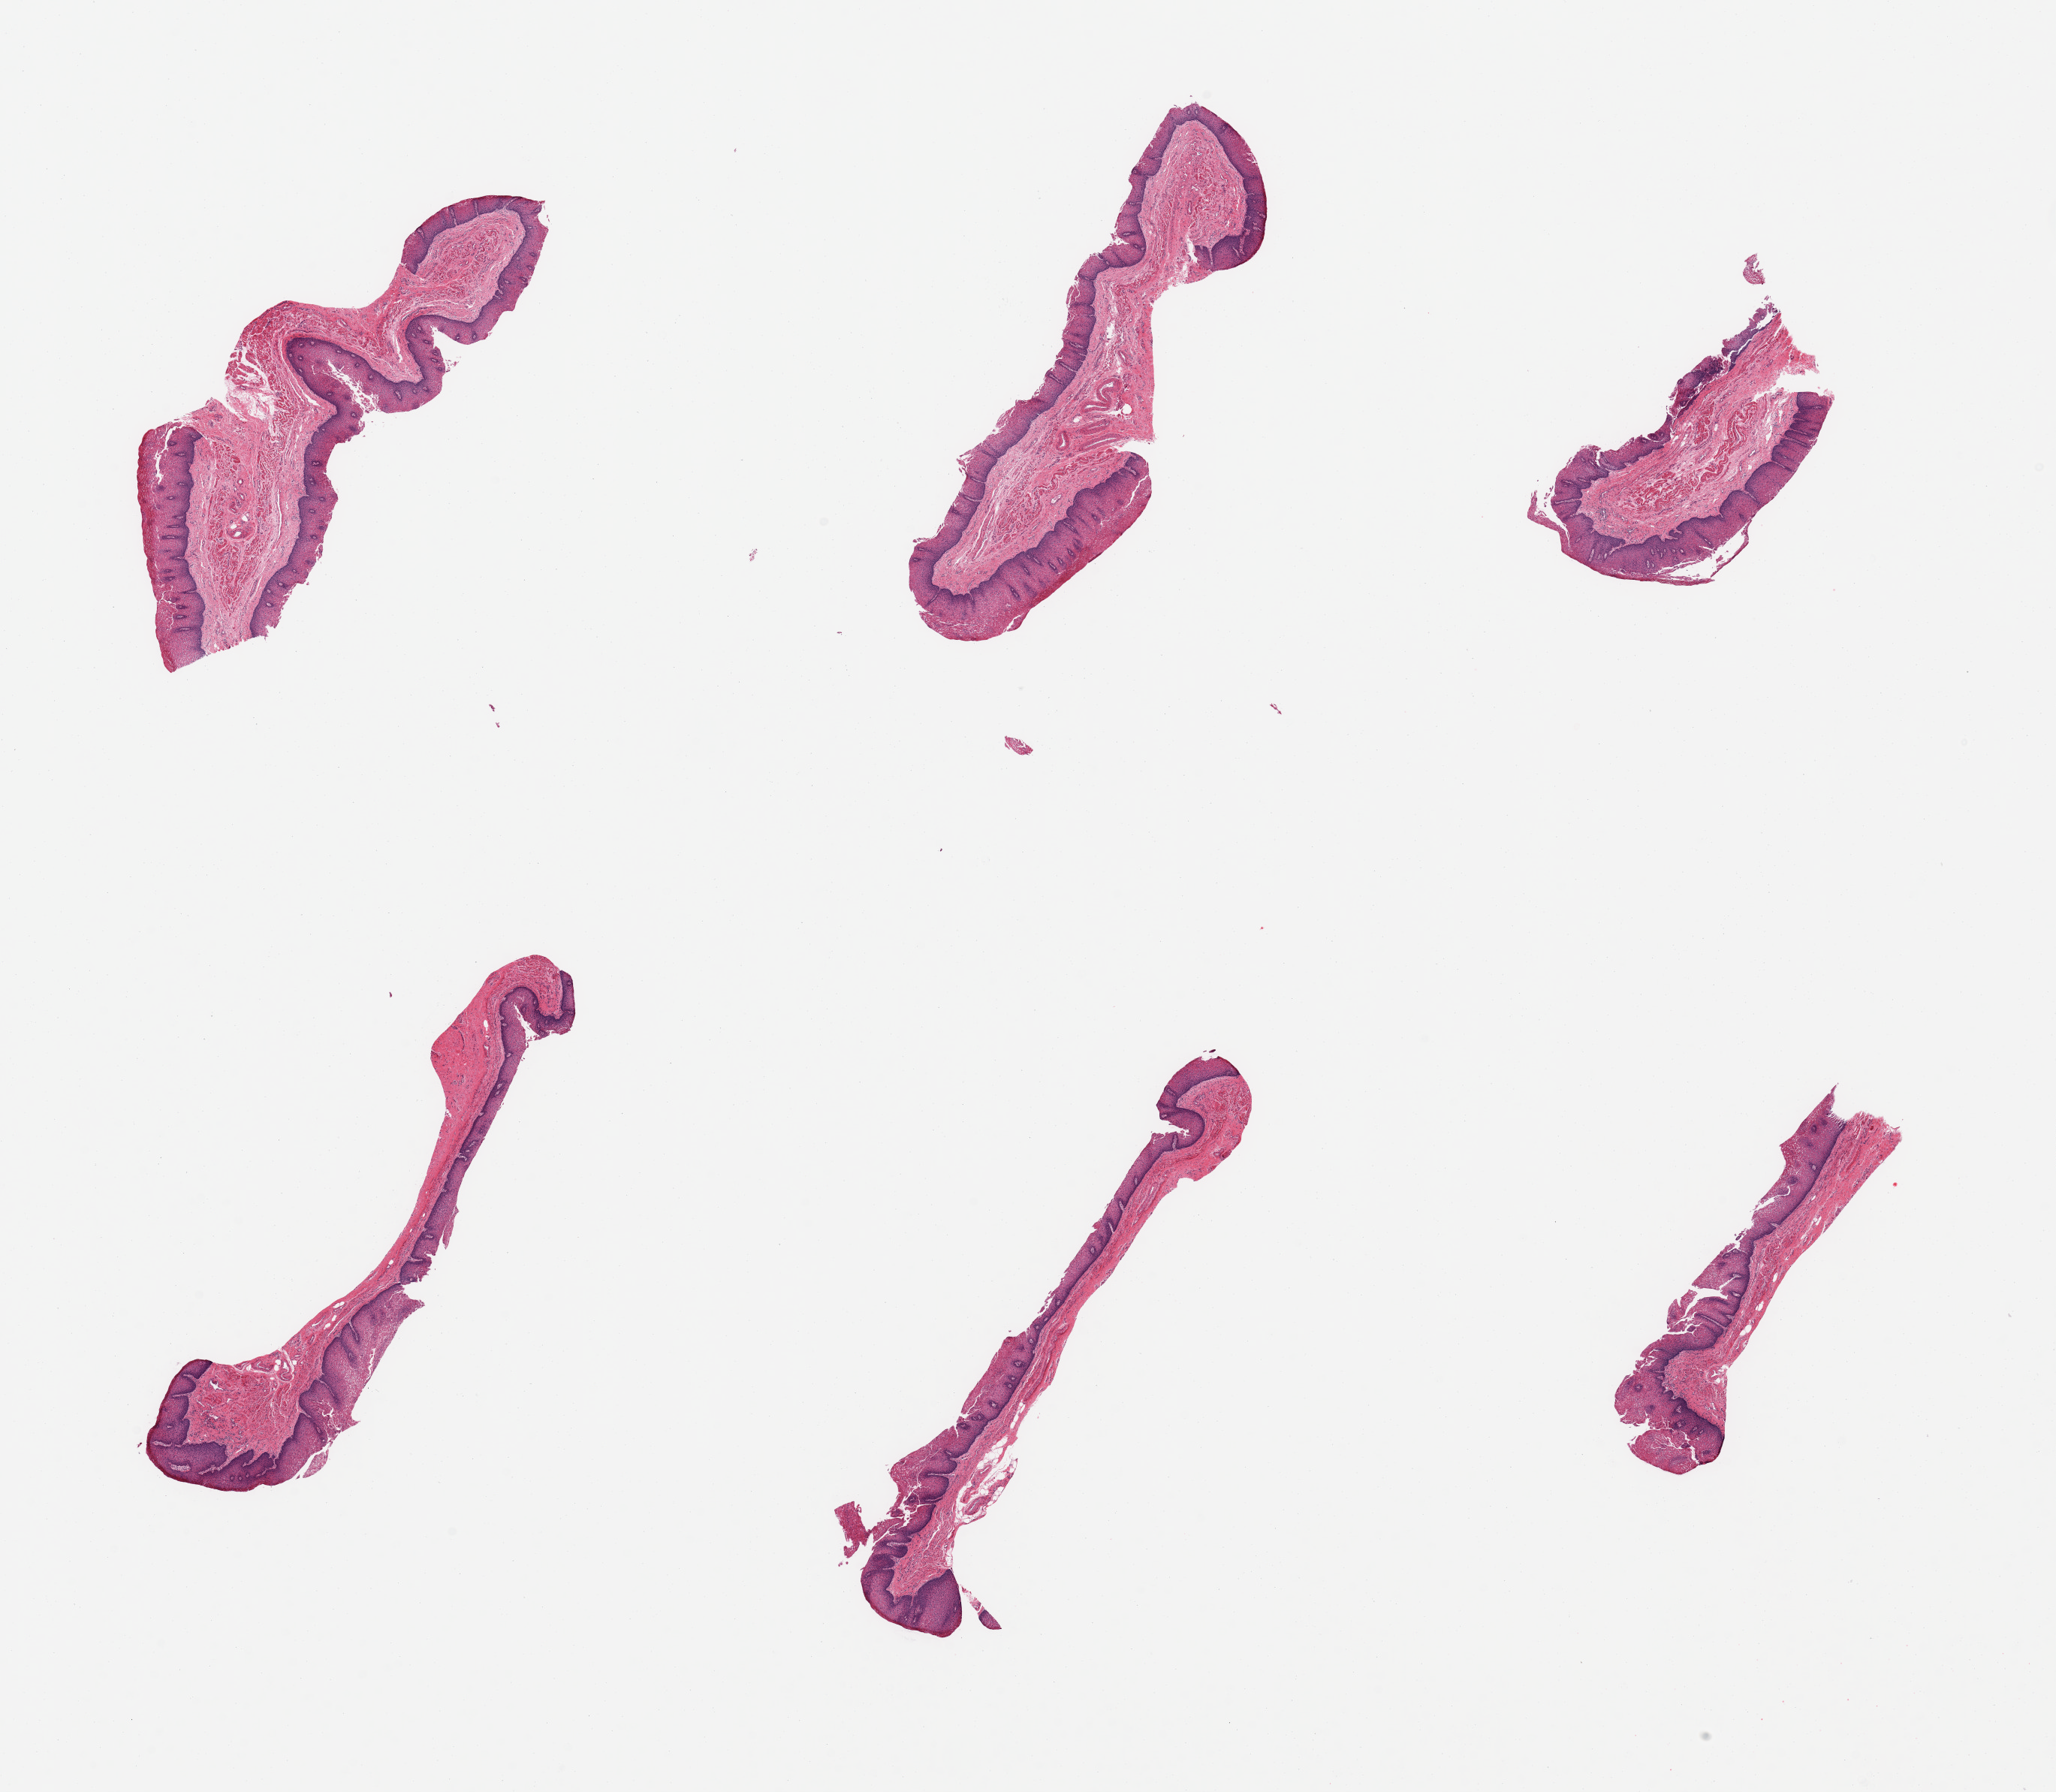
Whole-slide image, haematoxylin and eosin stain, whole scanned area (about 21.7 x 18.9 mm, acquisition: 20x scan) shown as a low-resolution overview; PAXgene-fixed paraffin-embedded (PFPE) section; target tissue: esophageal mucous membrane; donor tissue sample.
- review note (as recorded): 6 pieces